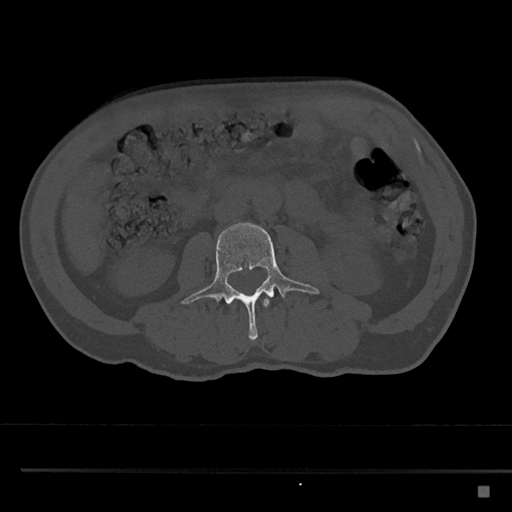
CT including the spine, one axial slice; position 701 of 797 along the scan axis; reconstruction kernel Br40s/3; 120 kVp; bone window (W 1800 / L 400 HU); 0.5 mm slice thickness; 512 × 512 image matrix. Male patient, age 59 years. Case-level facts recorded for this patient, not image findings: primary cancer: prostate.
Structures marked on this image (semi-automatically segmented with operator editing):
- L2 vertebra: bounding box [x1, y1, x2, y2] px = [227, 299, 269, 307]
- L3 vertebra: [181, 222, 320, 342]